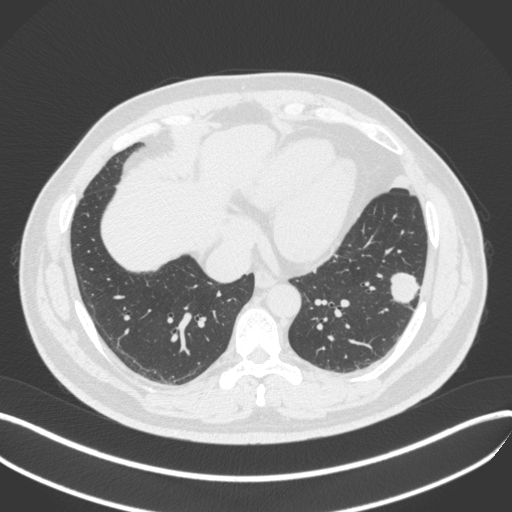
Chest CT, one axial slice. Slice 139 of 420 in the series (ordered by position). Reconstruction kernel B31f. Lung window (W 1500 / L -600 HU). 1 mm slice thickness. 512 × 512 image matrix. Patient: male, 39 years. From the clinical record (not read from this slice): clinical TNM (as recorded): T2a N0 M0.
Annotated regions visible in this slice (bounding box drawn by a radiologist):
- lung tumour (recorded histology: adenocarcinoma): box from (x=387, y=265) to (x=423, y=307) px